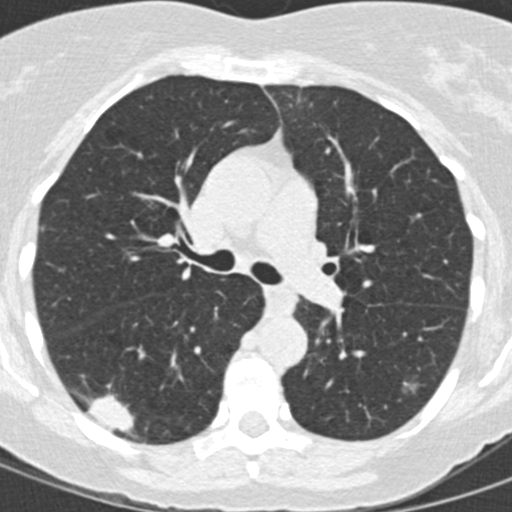
Low-dose screening chest CT, one axial slice; slice 89 of 146 in the series (ordered by position); lung window (W 1500 / L -600 HU); 2 mm slice thickness; 512 × 512 image matrix, field of view 270 × 270 mm.
Annotated regions visible in this slice (outlined manually by an expert reader):
- lesion 1 (tumor, lower lobe of right lung): box from (x=87, y=394) to (x=134, y=434) px